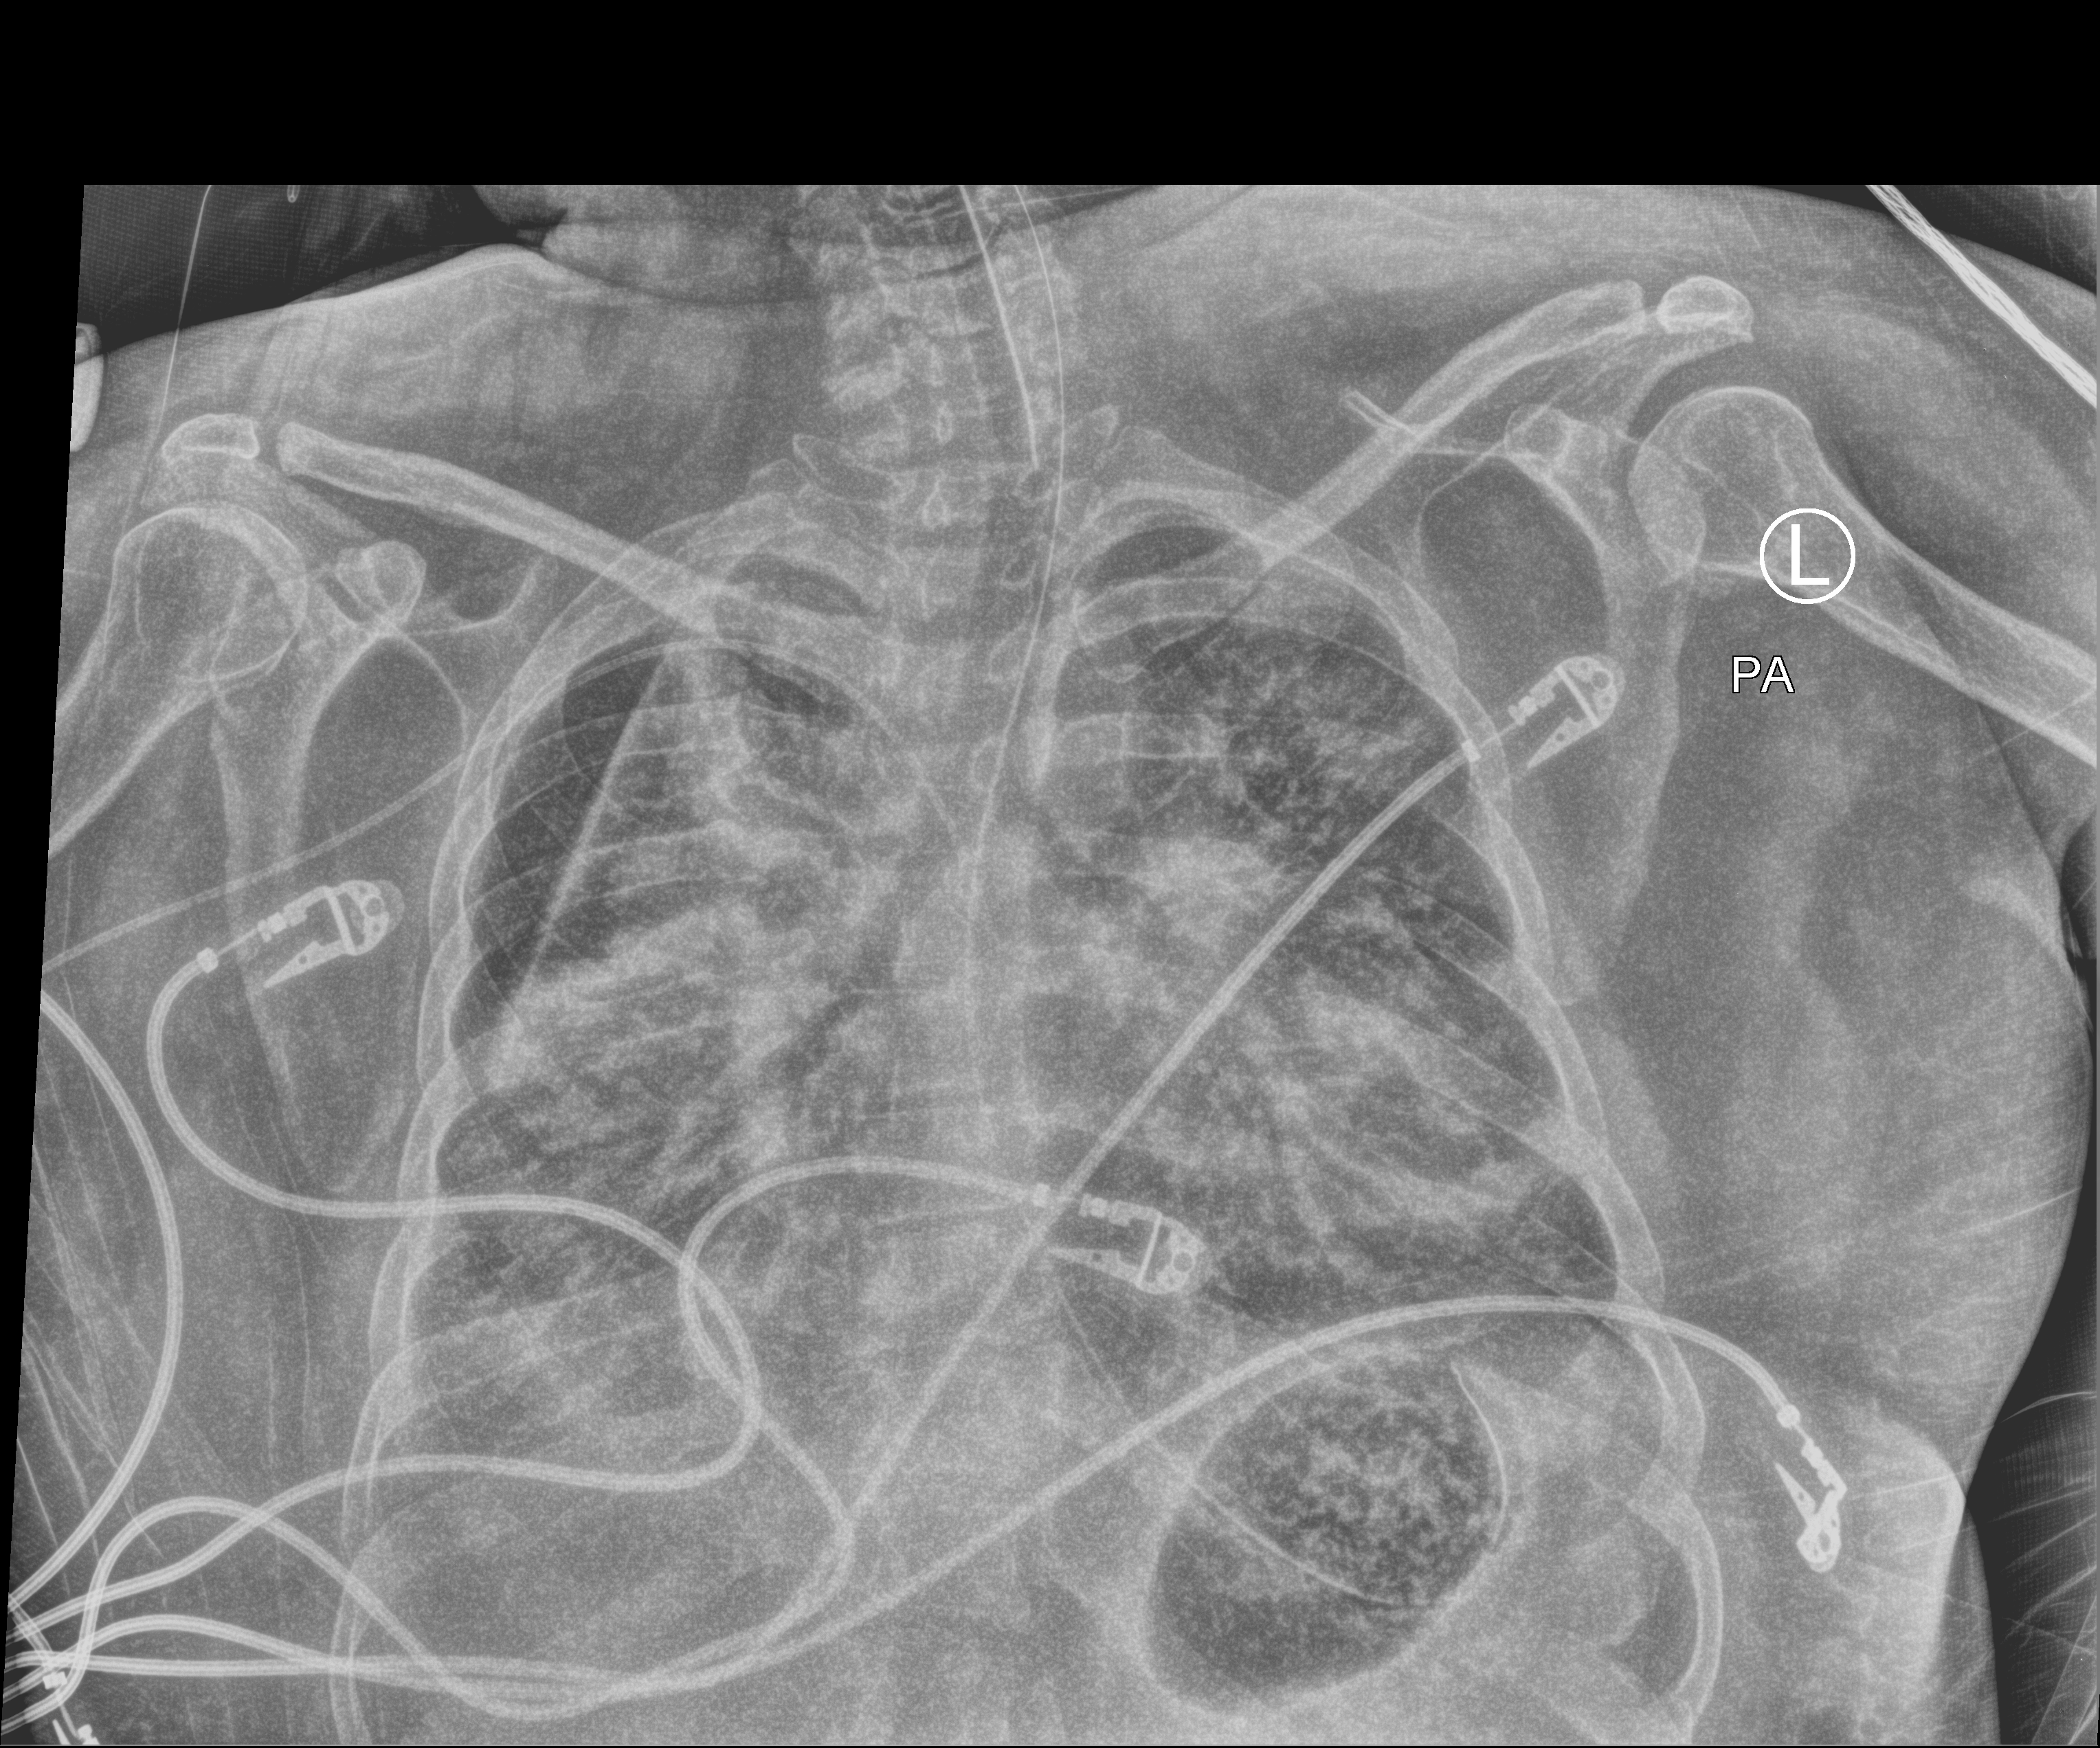
Portable chest radiograph. Patient hospitalised with COVID-19, aged 18–59 years.
From the hospital-stay record, not from the radiograph (when in the stay this image was taken is not recorded):
- admitted to intensive care during this hospital stay: yes
- mechanically ventilated during this hospital stay: yes